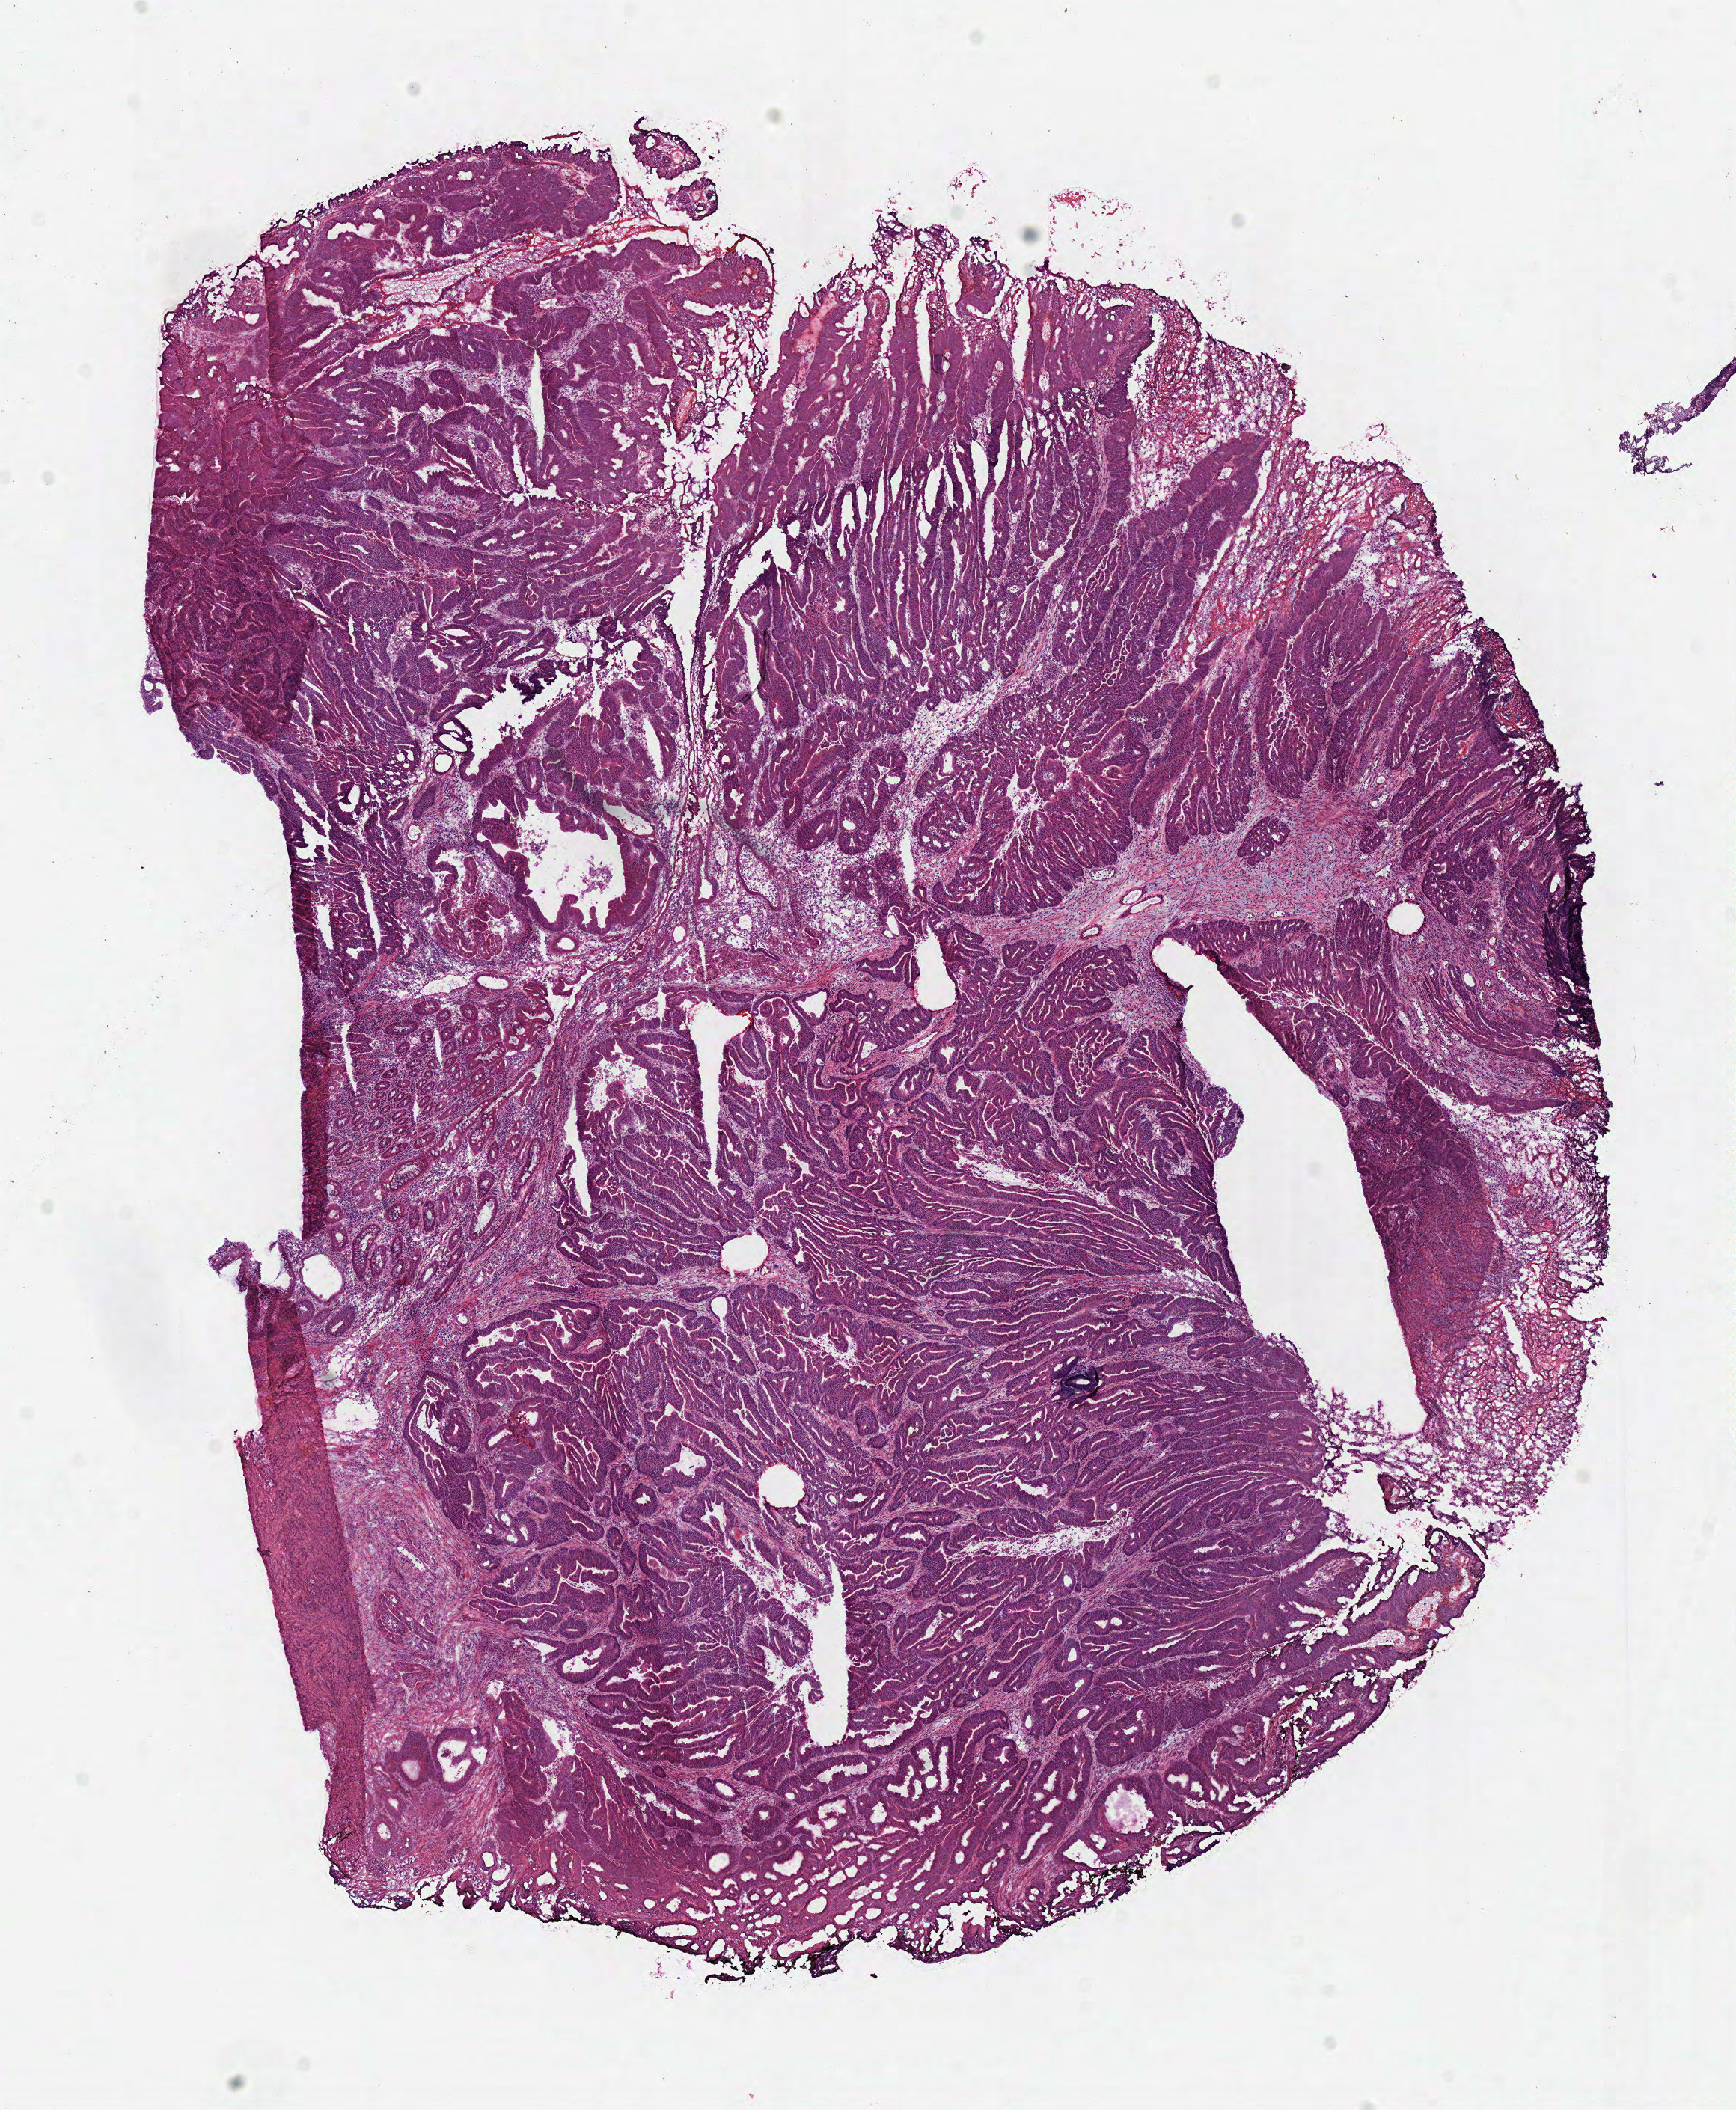
Hematoxylin and eosin (H&E) stained whole-slide image, shown as a low-resolution overview of the whole scanned area (about 9.1 x 11.1 mm, acquisition: 40x scan), frozen section from the top of the tissue portion, primary tumour sample from the colon. Male patient; age at initial diagnosis 76 years. Pathologist review of this section (percent, as recorded): tumour cells 80%, tumour nuclei 80%, normal cells 5%, stromal cells 10%, necrosis 5%. Inflammatory infiltration, as recorded: lymphocyte infiltration 15%.
Lymph nodes positive (case pathology): 0 of 16 examined. AJCC pathologic stage: IIA (6th edition). Pathologic diagnosis: Adenocarcinoma, NOS (ascending colon).